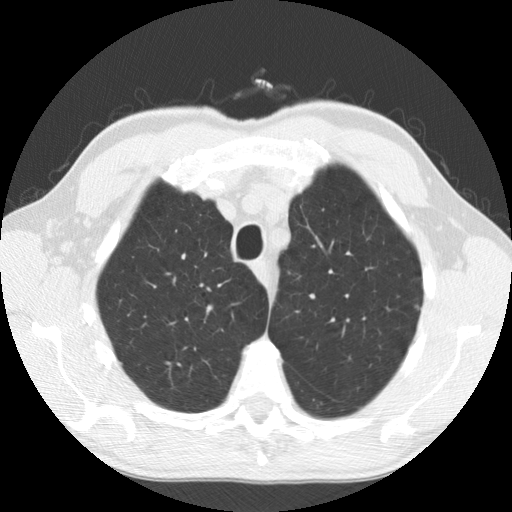
Chest CT (low-dose screening protocol), one axial image. Baseline screening round. Lung window (W 1500 / L -600 HU). Male participant, aged 63 years at enrolment. Current smoker at enrolment.
• Lesion marked by an expert reader, bounding box <400,293,435,326> (left, top, right, bottom; pixels).
• Screening reader's record for this exam: no non-calcified nodule ≥4 mm recorded.
• Official screen result: negative screen, minor abnormalities not suspicious for lung cancer.
• Later outcome: lung cancer diagnosed 858 days after this screen — adenocarcinoma, NOS, left upper lobe, well differentiated (G1), stage IB (AJCC 6th edition), 5 mm at pathology.